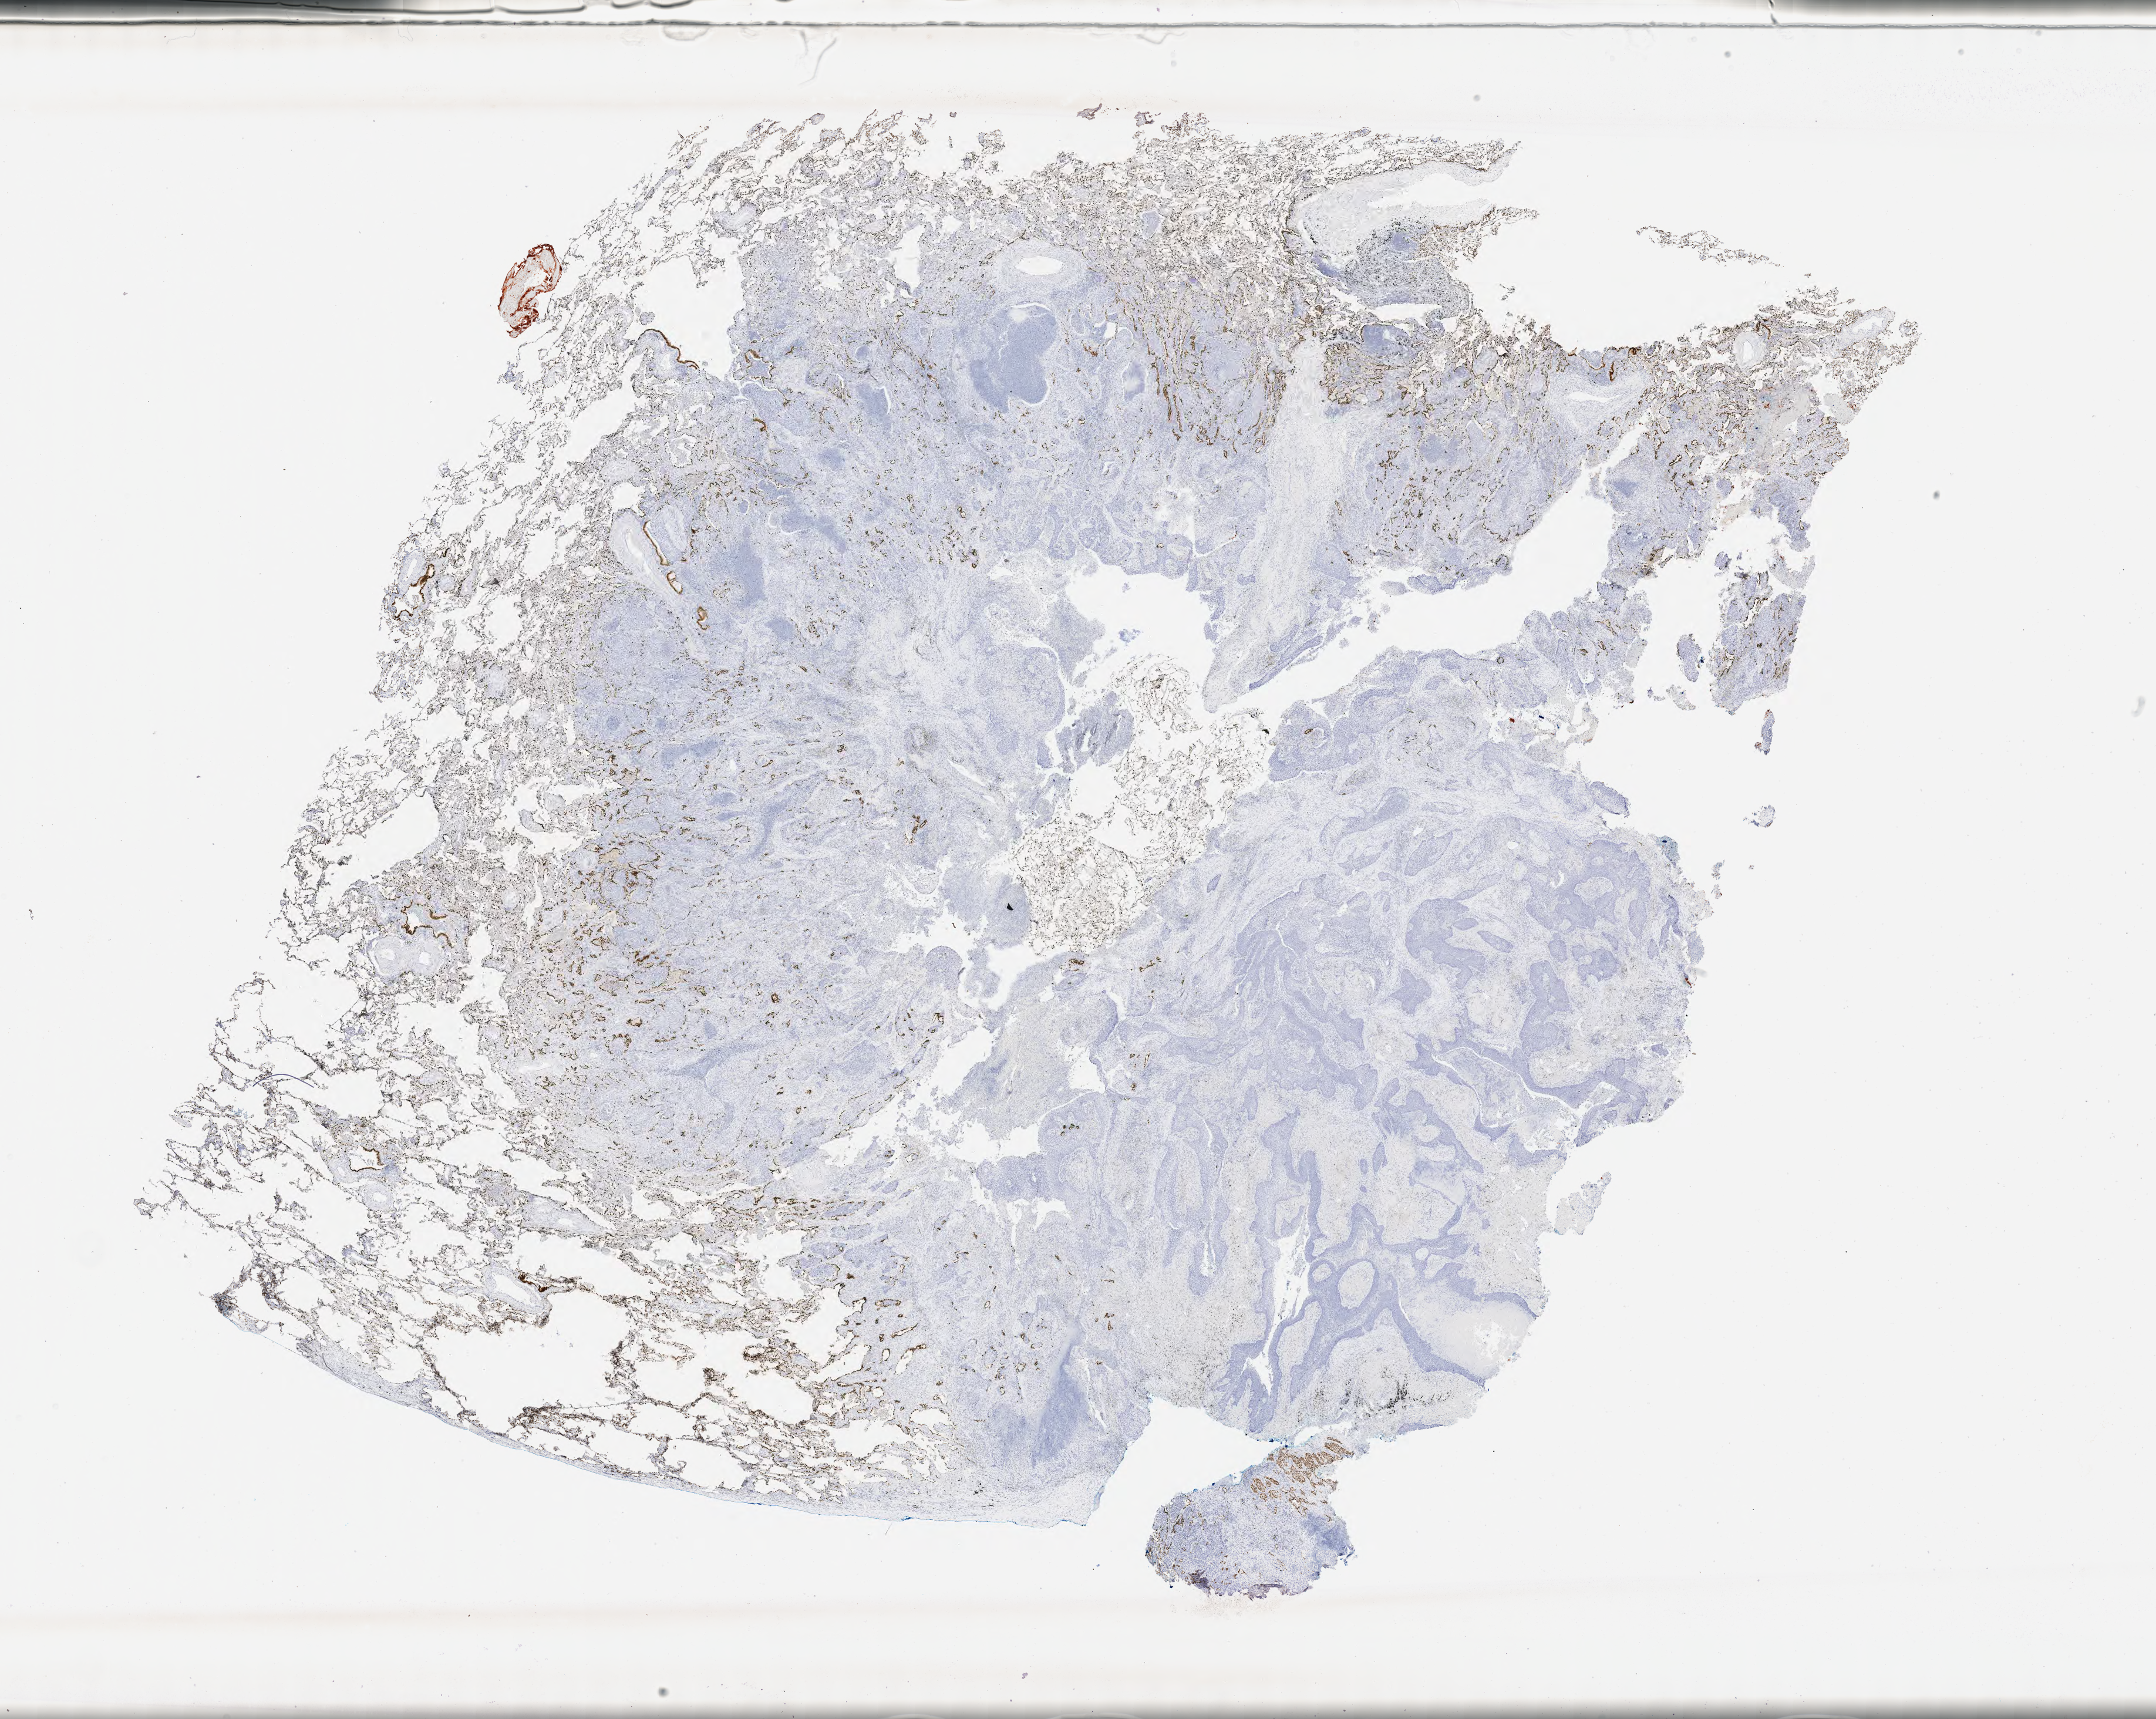
IHC for TTF-1 (thyroid transcription factor 1), whole-slide image, low-resolution overview of the scanned area, about 29.7 x 23.7 mm. Specimen: tumor tissue. Anatomic site: lung. Patient sex: male.
Diagnosis: Squamous cell carcinoma, NOS.